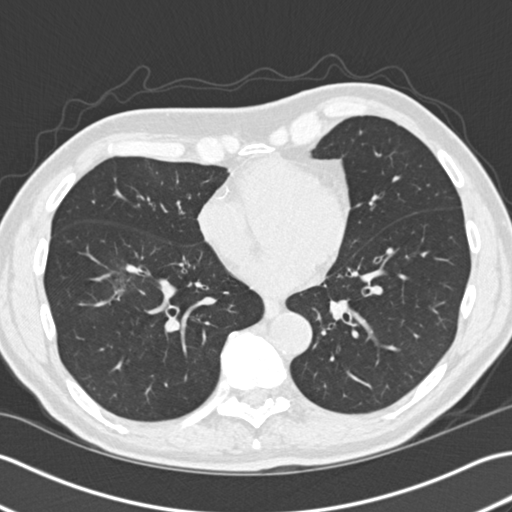
Low-dose screening chest CT, one axial slice. Position 66 of 172 along the scan axis. Reconstruction kernel B30f. 120 kVp. Lung window (W 1500 / L -600 HU). 2 mm slice thickness. 512 × 512 image matrix, field of view 350 × 350 mm.
Outlined on this slice (manually delineated by an expert):
- lesion 1 (tumor, lower lobe of right lung): bounding box <125,264,143,275> (left, top, right, bottom; pixels)